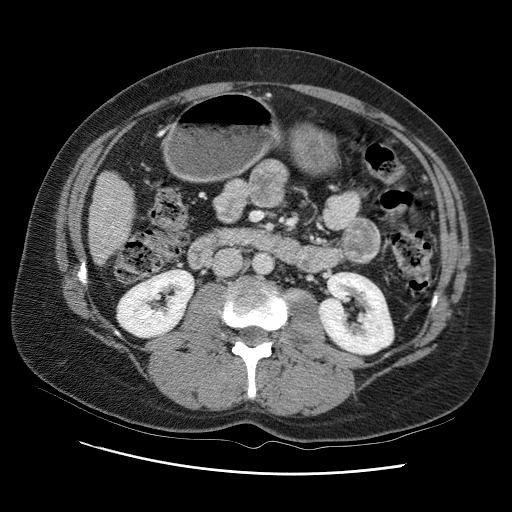
Contrast-enhanced abdominal CT (liver protocol), one axial slice. Position 24 of 95 along the scan axis. One of 2 acquisitions stored at this slice position. Soft-tissue window (W 400 / L 40 HU). 2.5 mm slice thickness. 512 × 512 image matrix, field of view 360 × 360 mm. From the clinical record (not read from this slice): diagnosis: hepatocellular carcinoma (patient treated with transarterial chemoembolisation; whether this scan precedes or follows treatment is not stated here); TNM stage (as recorded): Stage-I; Child-Pugh class: B; tumour differentiation: moderately differentiated; tumour nodularity: uninodular.
Outlined on this slice (semi-automatically segmented with operator editing):
- liver parenchyma outside the tumour (the mass and vessels are separate outlines, so this box may not span the whole liver): box from (x=90, y=154) to (x=146, y=266) px
- liver vessels: (x=114, y=196)–(x=122, y=218)